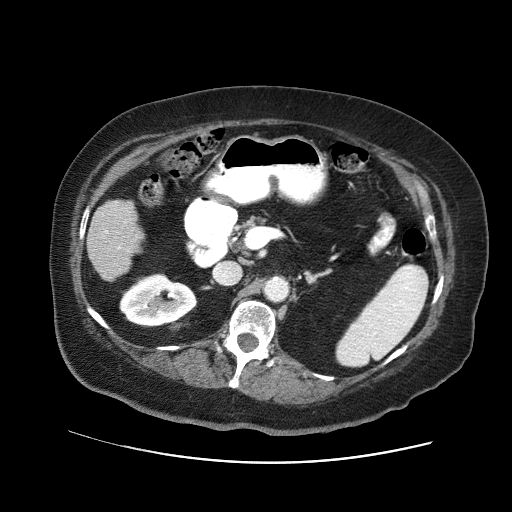
Contrast-enhanced abdominal CT (liver protocol), one axial slice. Slice 15 of 71 in the series (ordered by position). Reconstruction kernel STANDARD. 120 kVp. Soft-tissue window (W 400 / L 40 HU). 2.5 mm slice thickness. 512 × 512 image matrix, field of view 400 × 400 mm. From the clinical record (not read from this slice): diagnosis: hepatocellular carcinoma (patient treated with transarterial chemoembolisation; whether this scan precedes or follows treatment is not stated here); TNM stage (as recorded): Stage-II; Child-Pugh class: A; tumour nodularity: multinodular; tumour size: 5 cm.
Outlined on this slice (semi-automatically segmented with operator editing):
- liver parenchyma outside the tumour (the mass and vessels are separate outlines, so this box may not span the whole liver): bounding box [x1, y1, x2, y2] px = [86, 200, 142, 280]
- liver vessels: [105, 231, 108, 233]